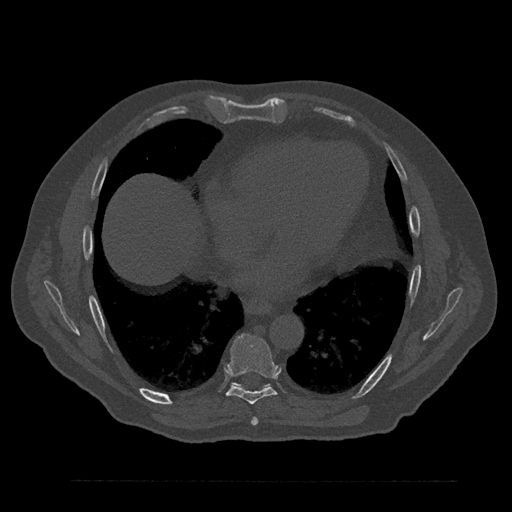
CT including the spine, one axial slice; position 448 of 797 along the scan axis; bone window (W 1800 / L 400 HU); 0.5 mm slice thickness; 512 × 512 image matrix, field of view 430 × 430 mm. Male patient, age 61 years. Case-level facts recorded for this patient, not image findings: primary cancer: prostate.
Annotated regions visible in this slice (semi-automatically segmented with operator editing):
- T7 vertebra: bounding box [x1, y1, x2, y2] px = [251, 417, 258, 426]
- T8 vertebra: [226, 334, 278, 405]
- T9 vertebra: [233, 383, 269, 386]